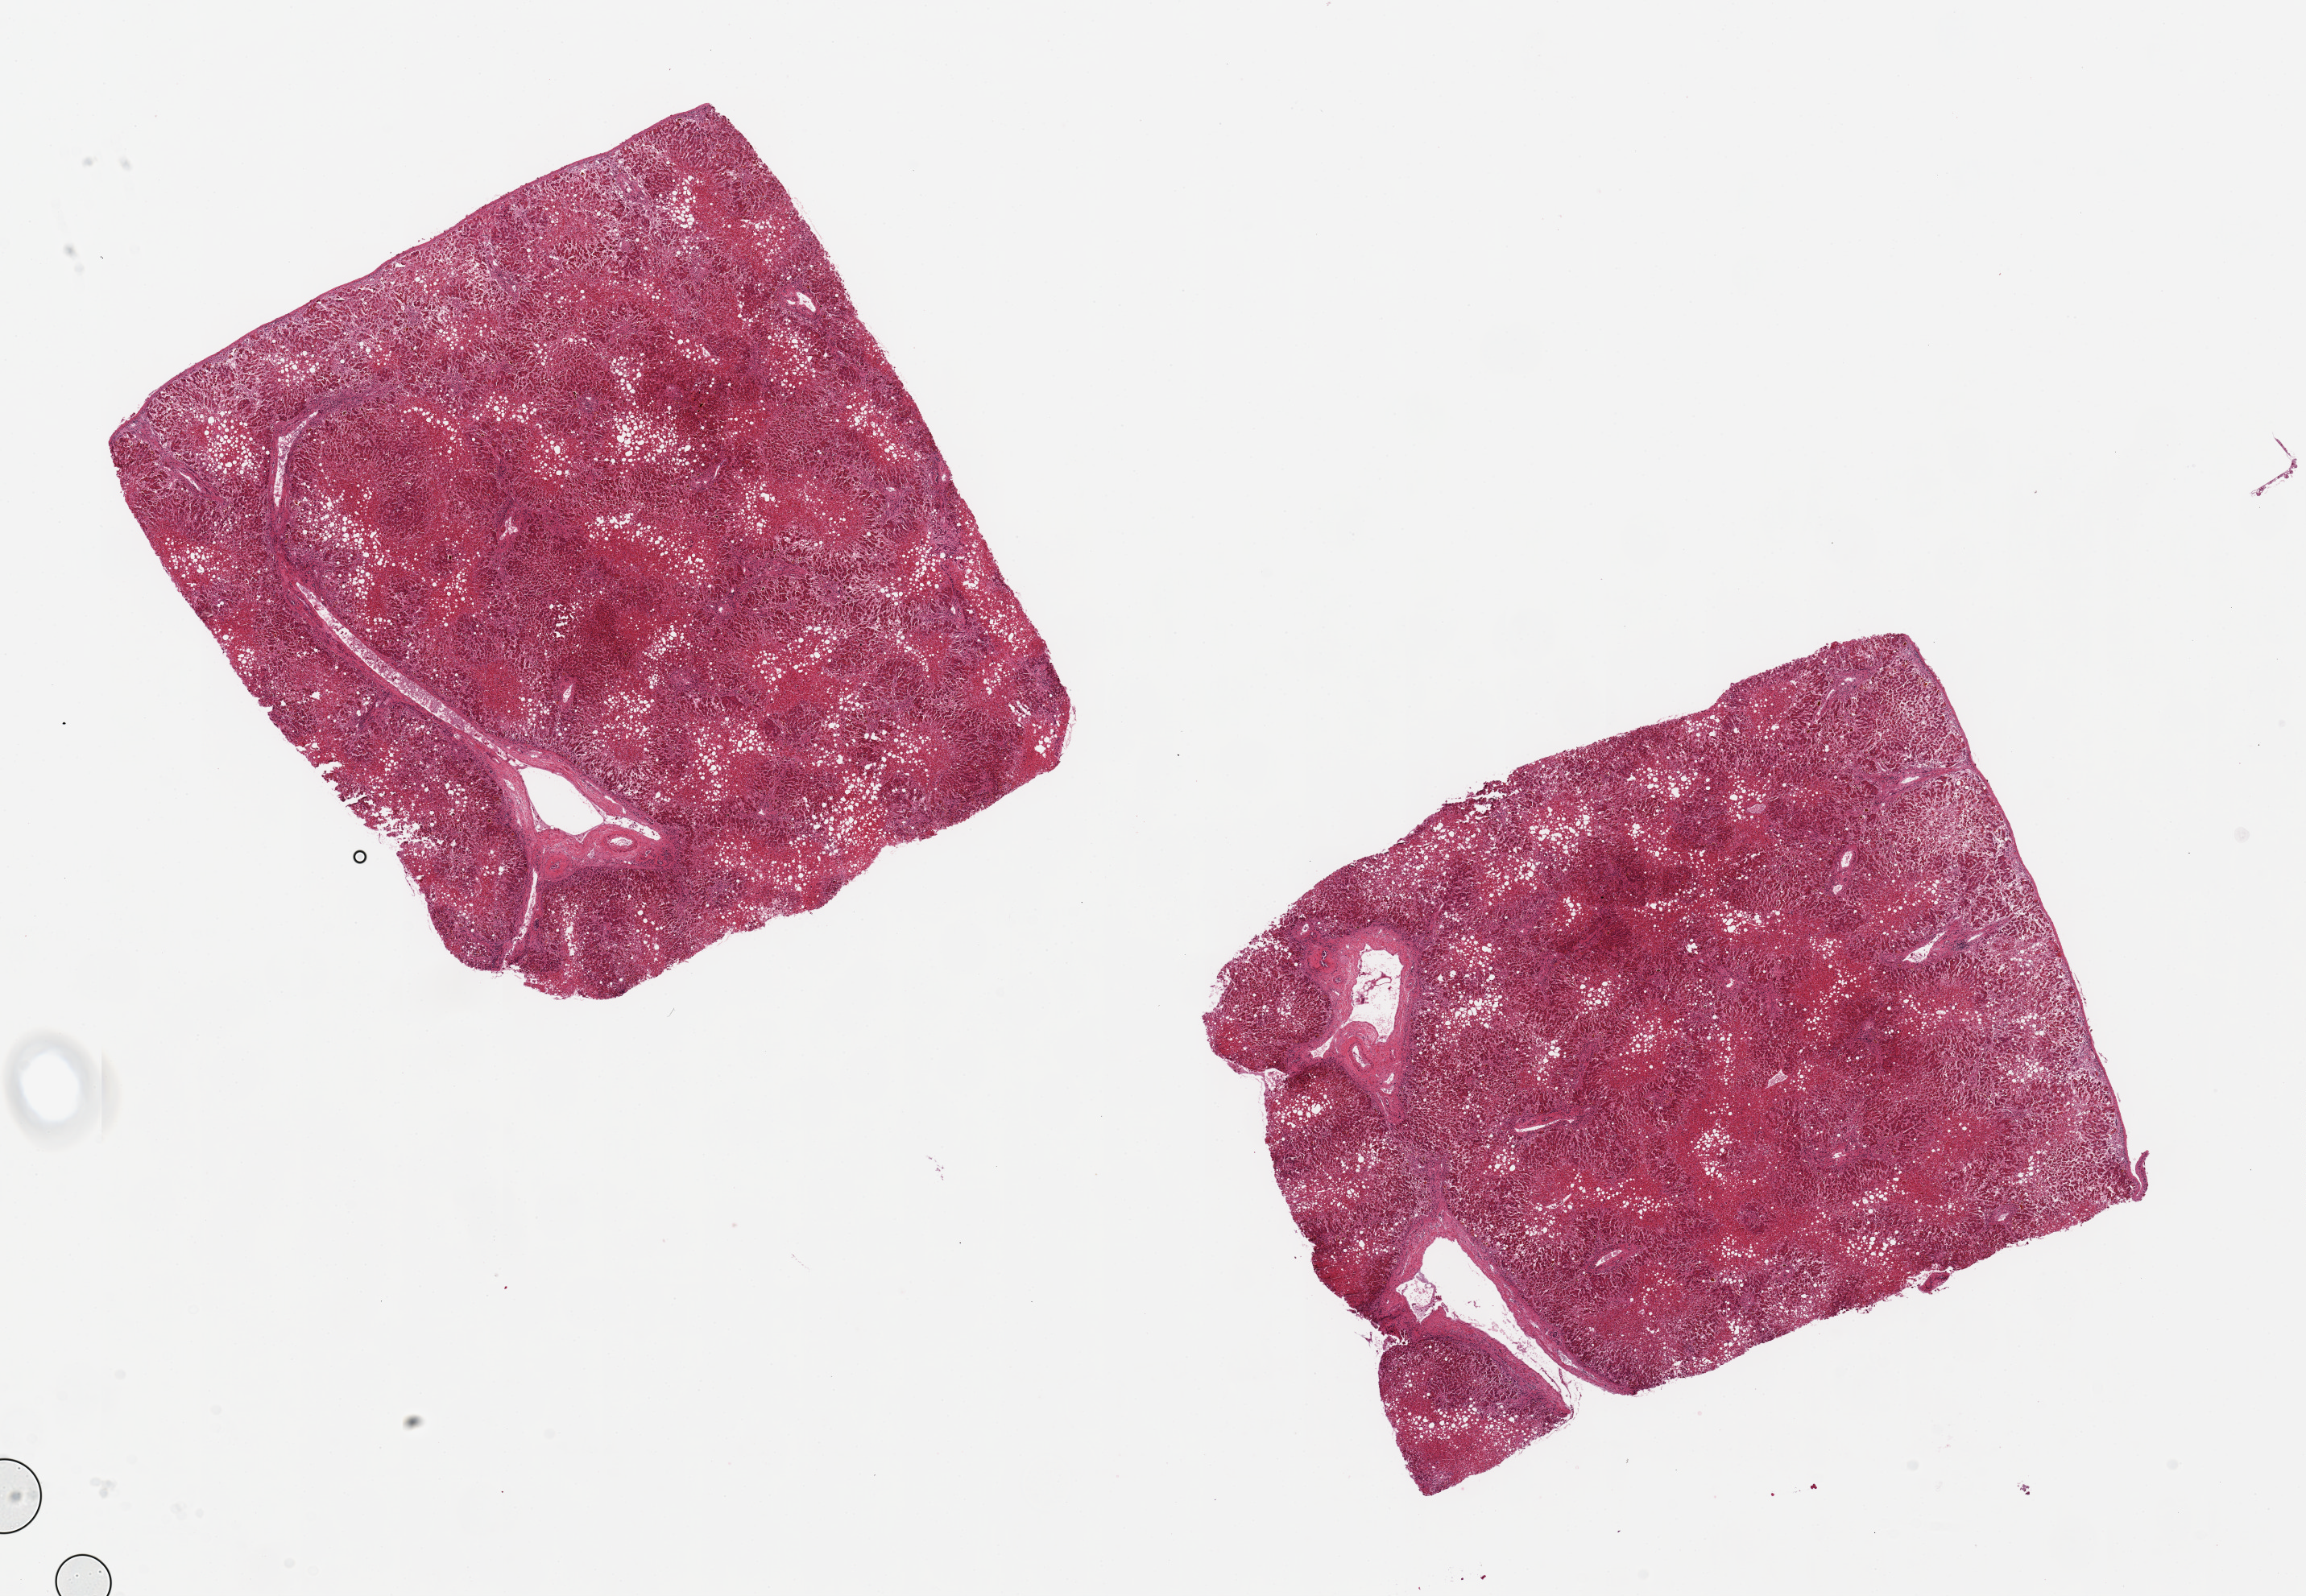
H&E whole-slide image — low-resolution overview of the scanned area, about 22.6 x 15.7 mm (from a 20x scan); PAXgene-fixed paraffin-embedded (PFPE) section; sampled site (target tissue): liver; tissue donor sample.
Pathologist's review note for this sample: 2 pieces badly autolyzed. ? cirrhosis but so necrotic impossible for definitive assessment.